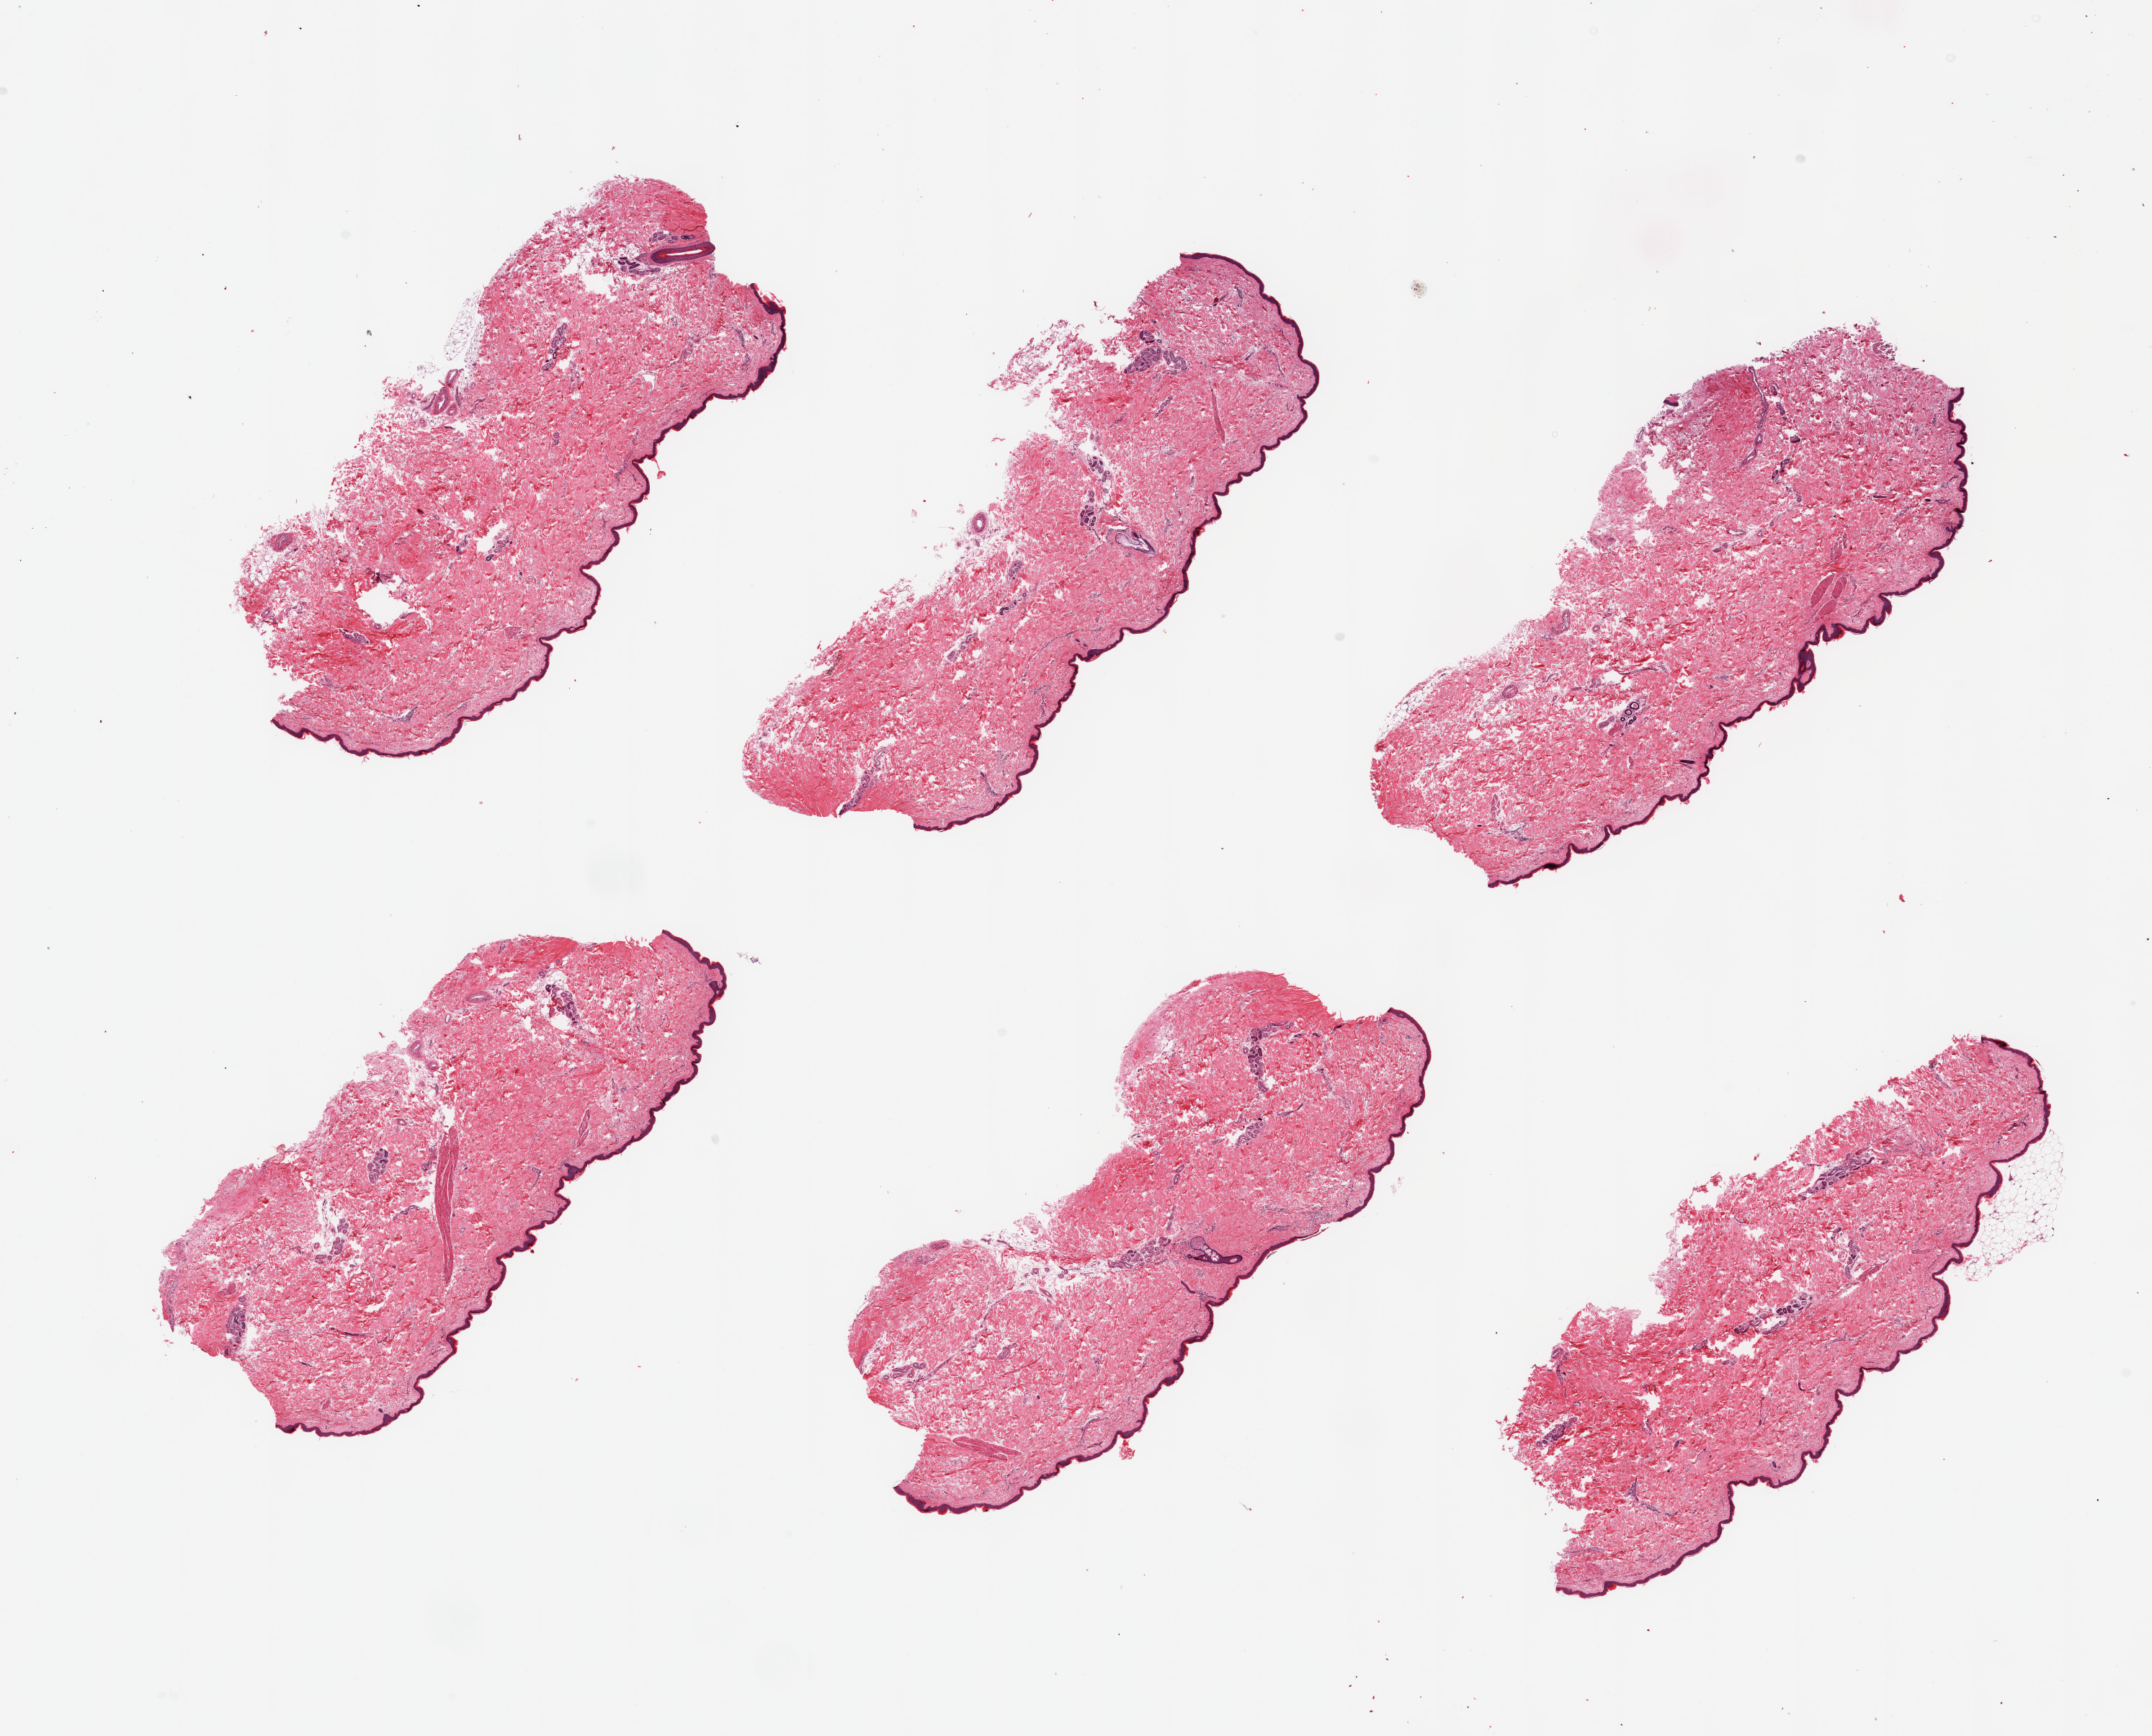
H&E whole-slide image — a low-resolution overview of the entire scanned area, about 23.6 x 19.1 mm. PAXgene-fixed, paraffin-embedded tissue. Sampled site (target tissue): skin of lower leg. Donor tissue sample. Male donor.
* pathologist's review note for this sample: 6 pieces, no dermal fat, squamous epithelium is ~50 microns